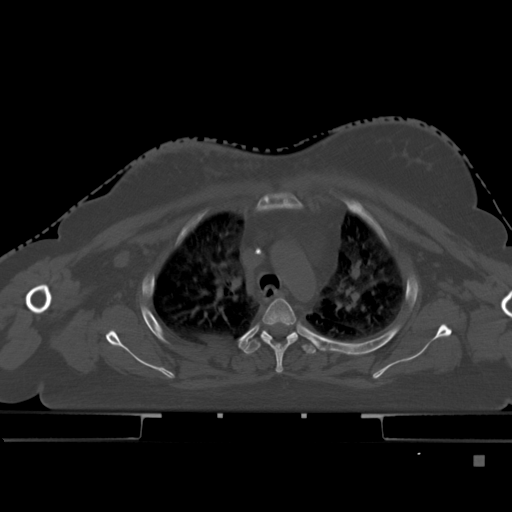
CT including the spine, one axial slice; position 340 of 495 along the scan axis; bone window (W 1800 / L 400 HU); 1.5 mm slice thickness; 512 × 512 image matrix, field of view 404 × 404 mm. Patient: female, 33 years. Case-level facts recorded for this patient, not image findings: primary cancer: breast.
Annotated regions visible in this slice (semi-automatic segmentation, software-assisted and operator-edited):
- T3 vertebra: bounding box <261,297,298,373> (left, top, right, bottom; pixels)
- T4 vertebra: <244,330,319,355>